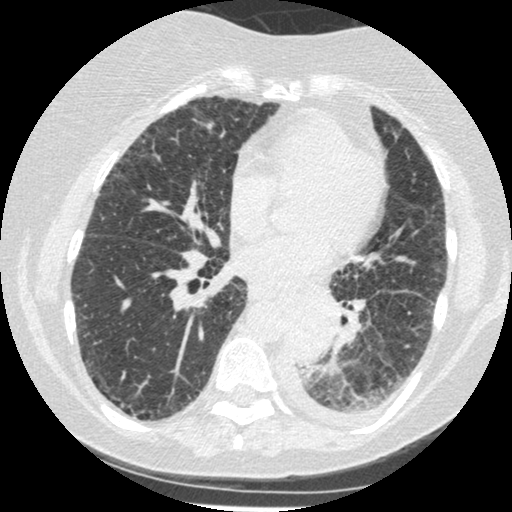
Chest CT (low-dose screening protocol), one axial image, third annual screen, lung window (W 1500 / L -600 HU), 1.25 mm slice thickness, 120 kVp, slice 241 of 341 in the series. Female participant, aged 60 years at enrolment.
Lesion marked by an expert reader, bounding box [x1, y1, x2, y2] px = [276, 303, 343, 376]. Reader record for this screening exam (exam-level; its link to the box is not recorded): non-calcified nodule or mass ≥4 mm, left lower lobe, 54 × 38 mm, smooth margins, soft tissue attenuation, pre-existing on the prior screen: yes; interval growth: yes. Official screen result: positive, other. Participant outcome: lung cancer diagnosed 15 days after this screen — small cell carcinoma, NOS, left lower lobe, undifferentiated (G4), stage IV (AJCC 6th edition), 69 mm at pathology.